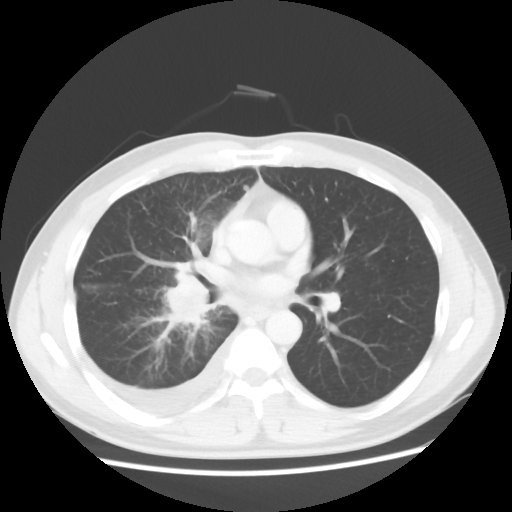
Chest CT, one axial slice; slice 29 of 56 in the series (ordered by position); reconstruction kernel STANDARD; 120 kVp; lung window (W 1500 / L -600 HU); 512 × 512 image matrix. Patient: male, 46 years. Case-level facts recorded for this patient, not image findings: clinical TNM (as recorded): T2 N3 M1.
Structures marked on this image (bounding box drawn by a radiologist):
- lung tumour (recorded histology: adenocarcinoma): bounding box [x1, y1, x2, y2] px = [165, 272, 210, 336]